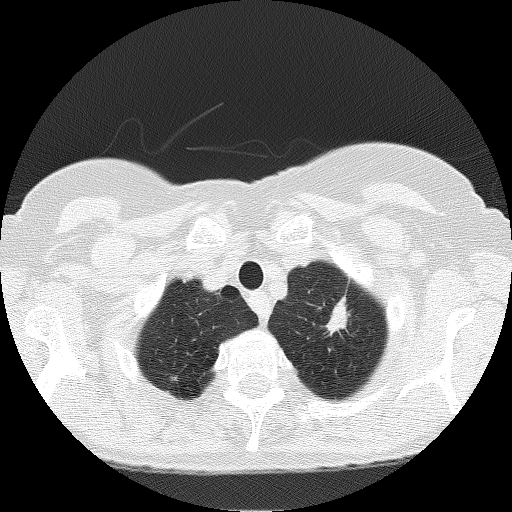
Low-dose screening chest CT, one axial slice; slice 152 of 166 in the series (ordered by position); reconstruction kernel FC51; 120 kVp; lung window (W 1500 / L -600 HU); 2 mm slice thickness; 512 × 512 image matrix, field of view 303 × 303 mm.
Outlined on this slice (expert manual segmentation):
- lesion 3 (nodule, upper lobe of left lung): bounding box (x1, y1, x2, y2) in pixels: (326, 300, 349, 333)